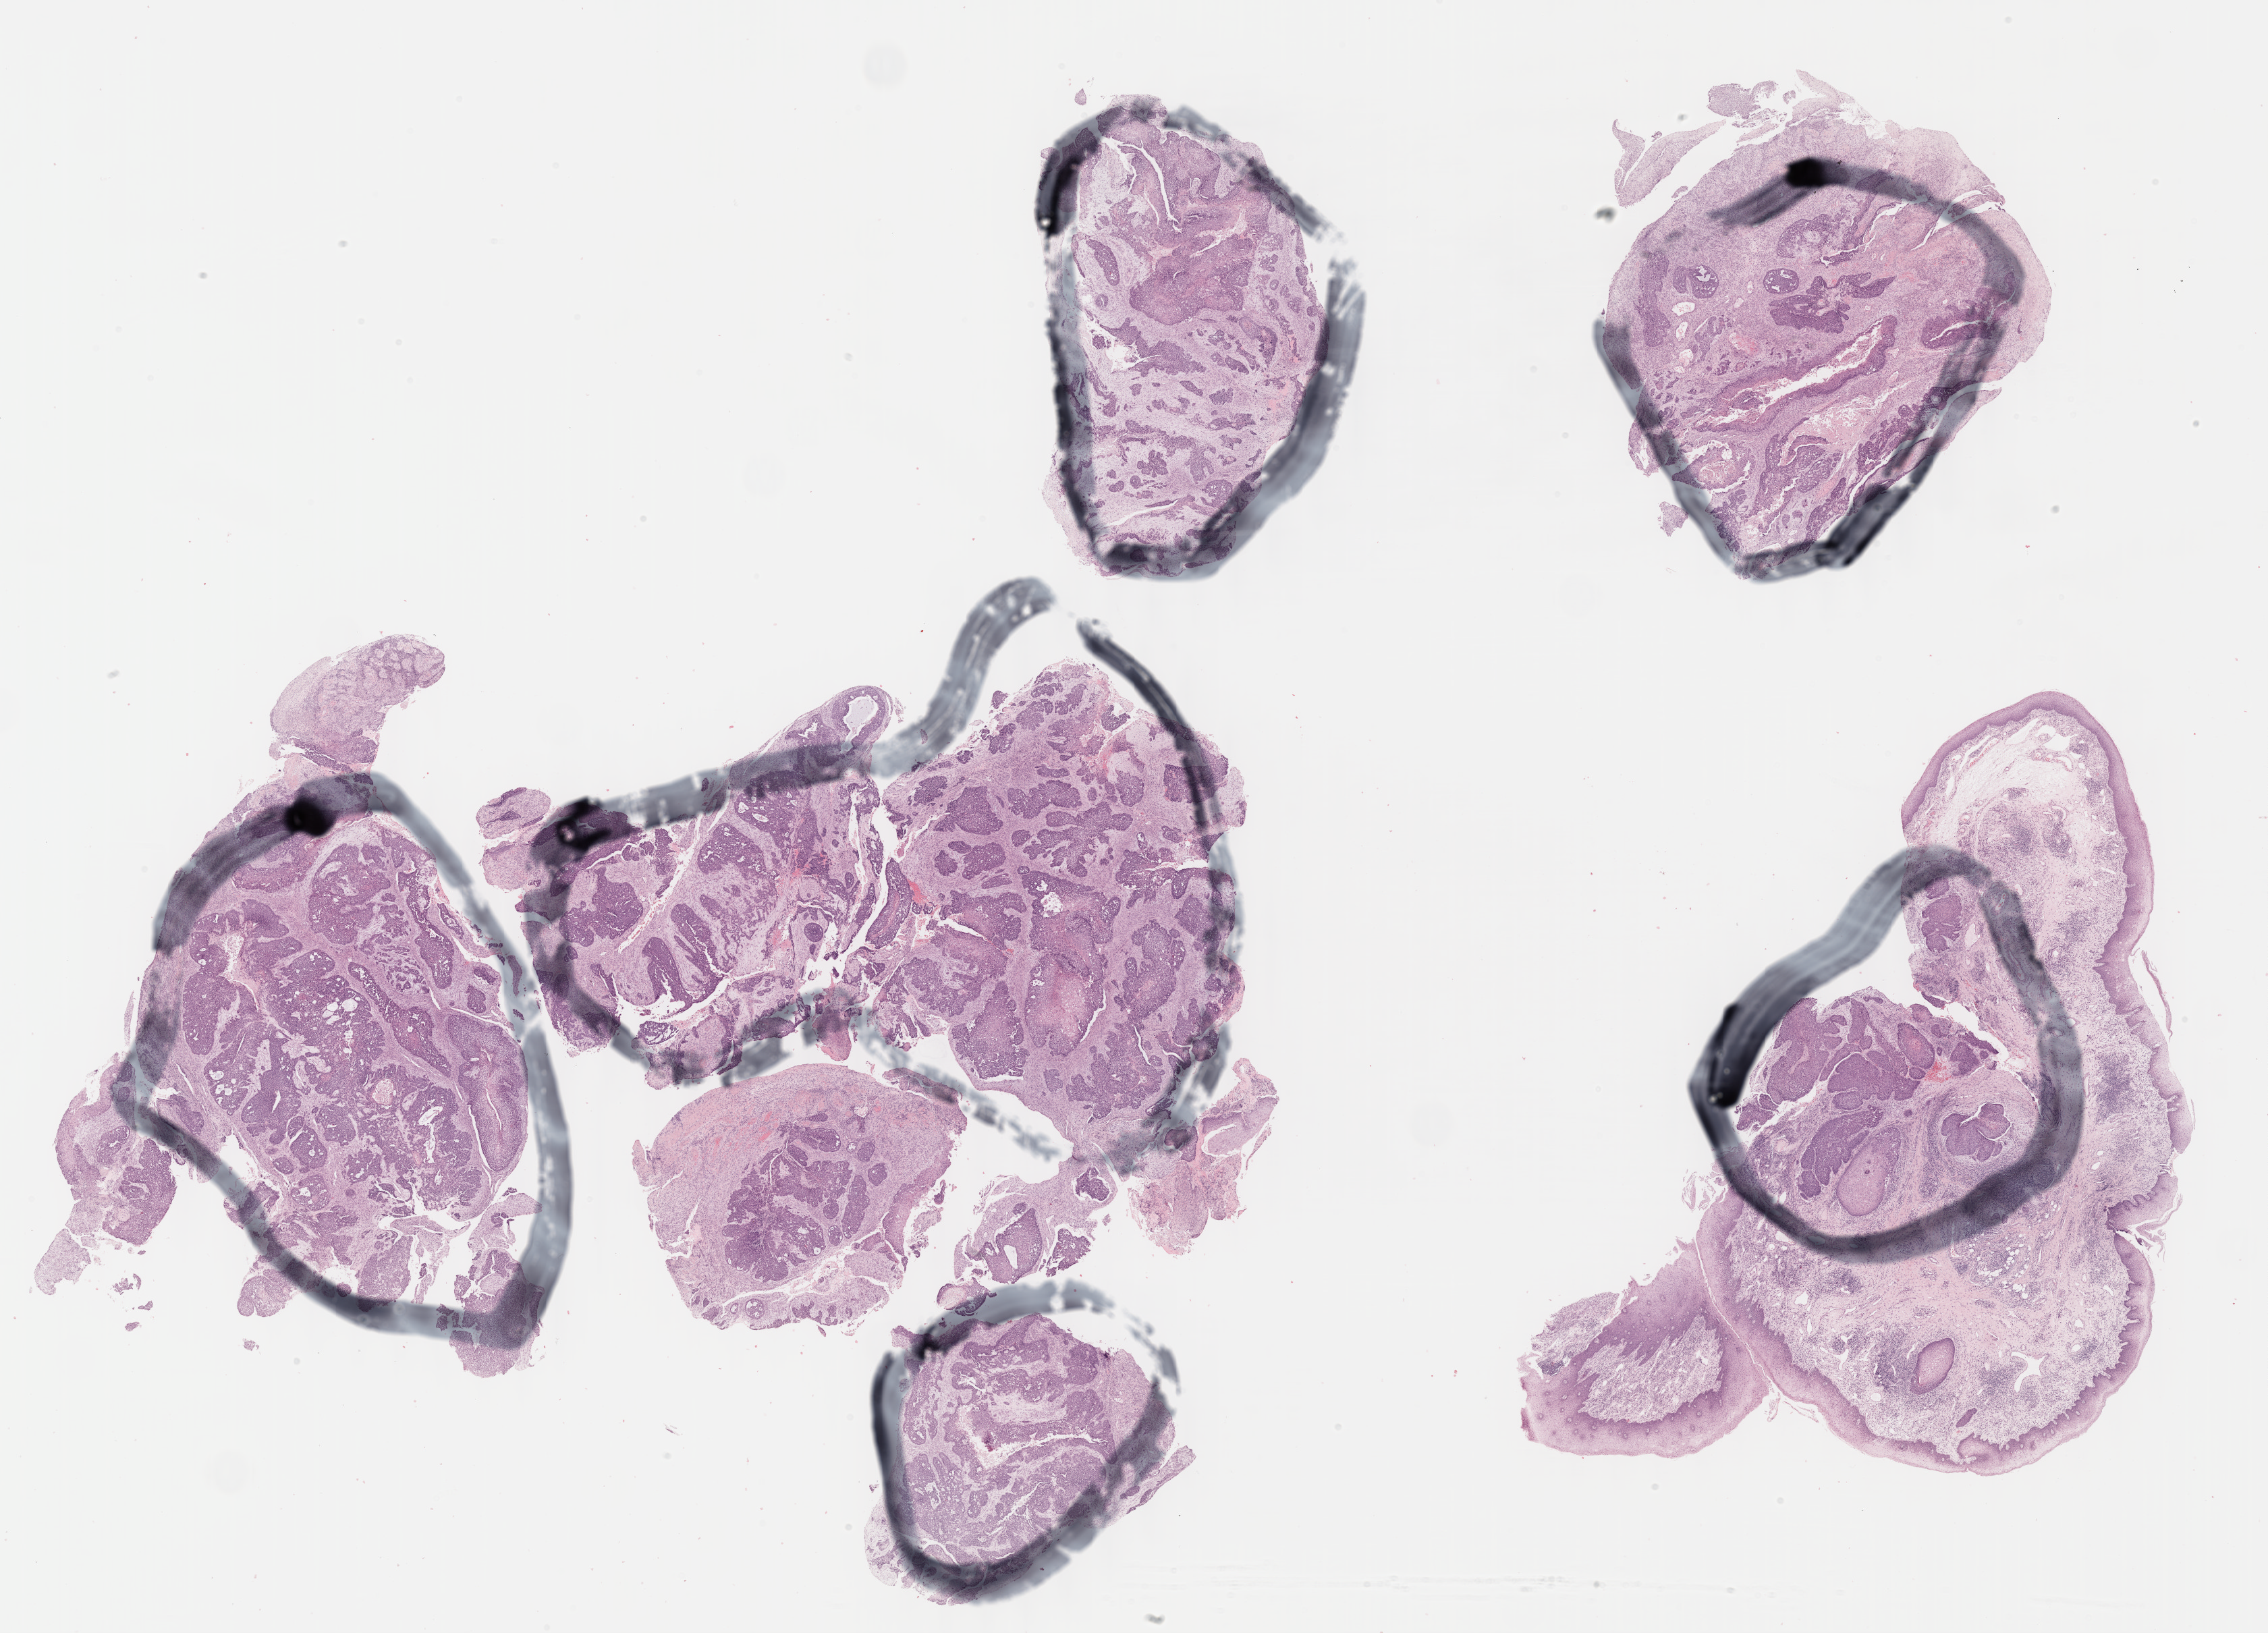
Digitized H&E-stained tissue section (whole slide), whole scanned area (about 27.2 x 19.6 mm, from a 40x scan) shown as a low-resolution overview. Formalin-fixed paraffin-embedded (FFPE) diagnostic section. Head and neck, primary tumour sample. Male, age 70 years at initial diagnosis.
Histologic diagnosis: Squamous cell carcinoma, NOS.